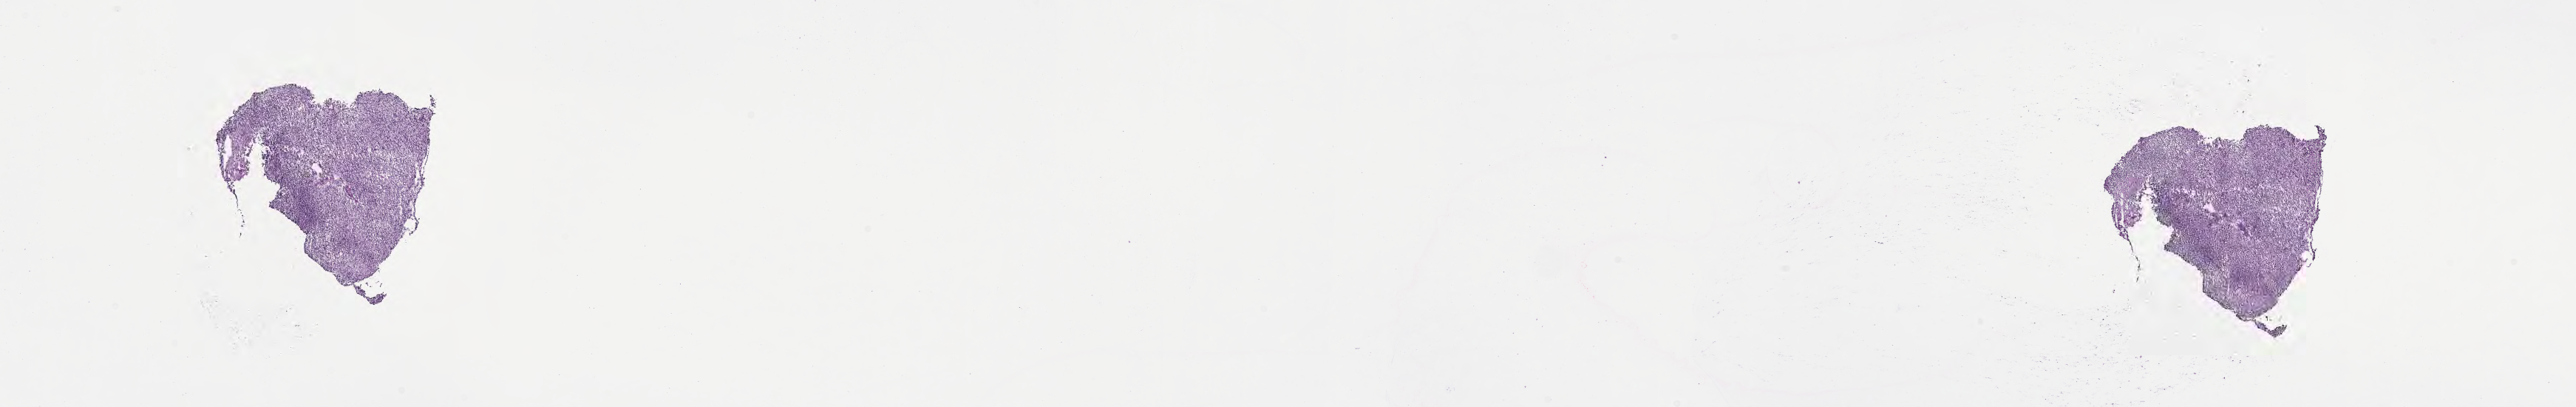
Digitized H&E-stained section of tumor tissue from the cerebellum — low-resolution overview of the scanned area, about 28.2 x 4.4 mm. Cryosection (OCT / tissue freezing medium). Male patient, age 82 months (6 years 10 months).
Diagnosis: Medulloblastoma, NOS.